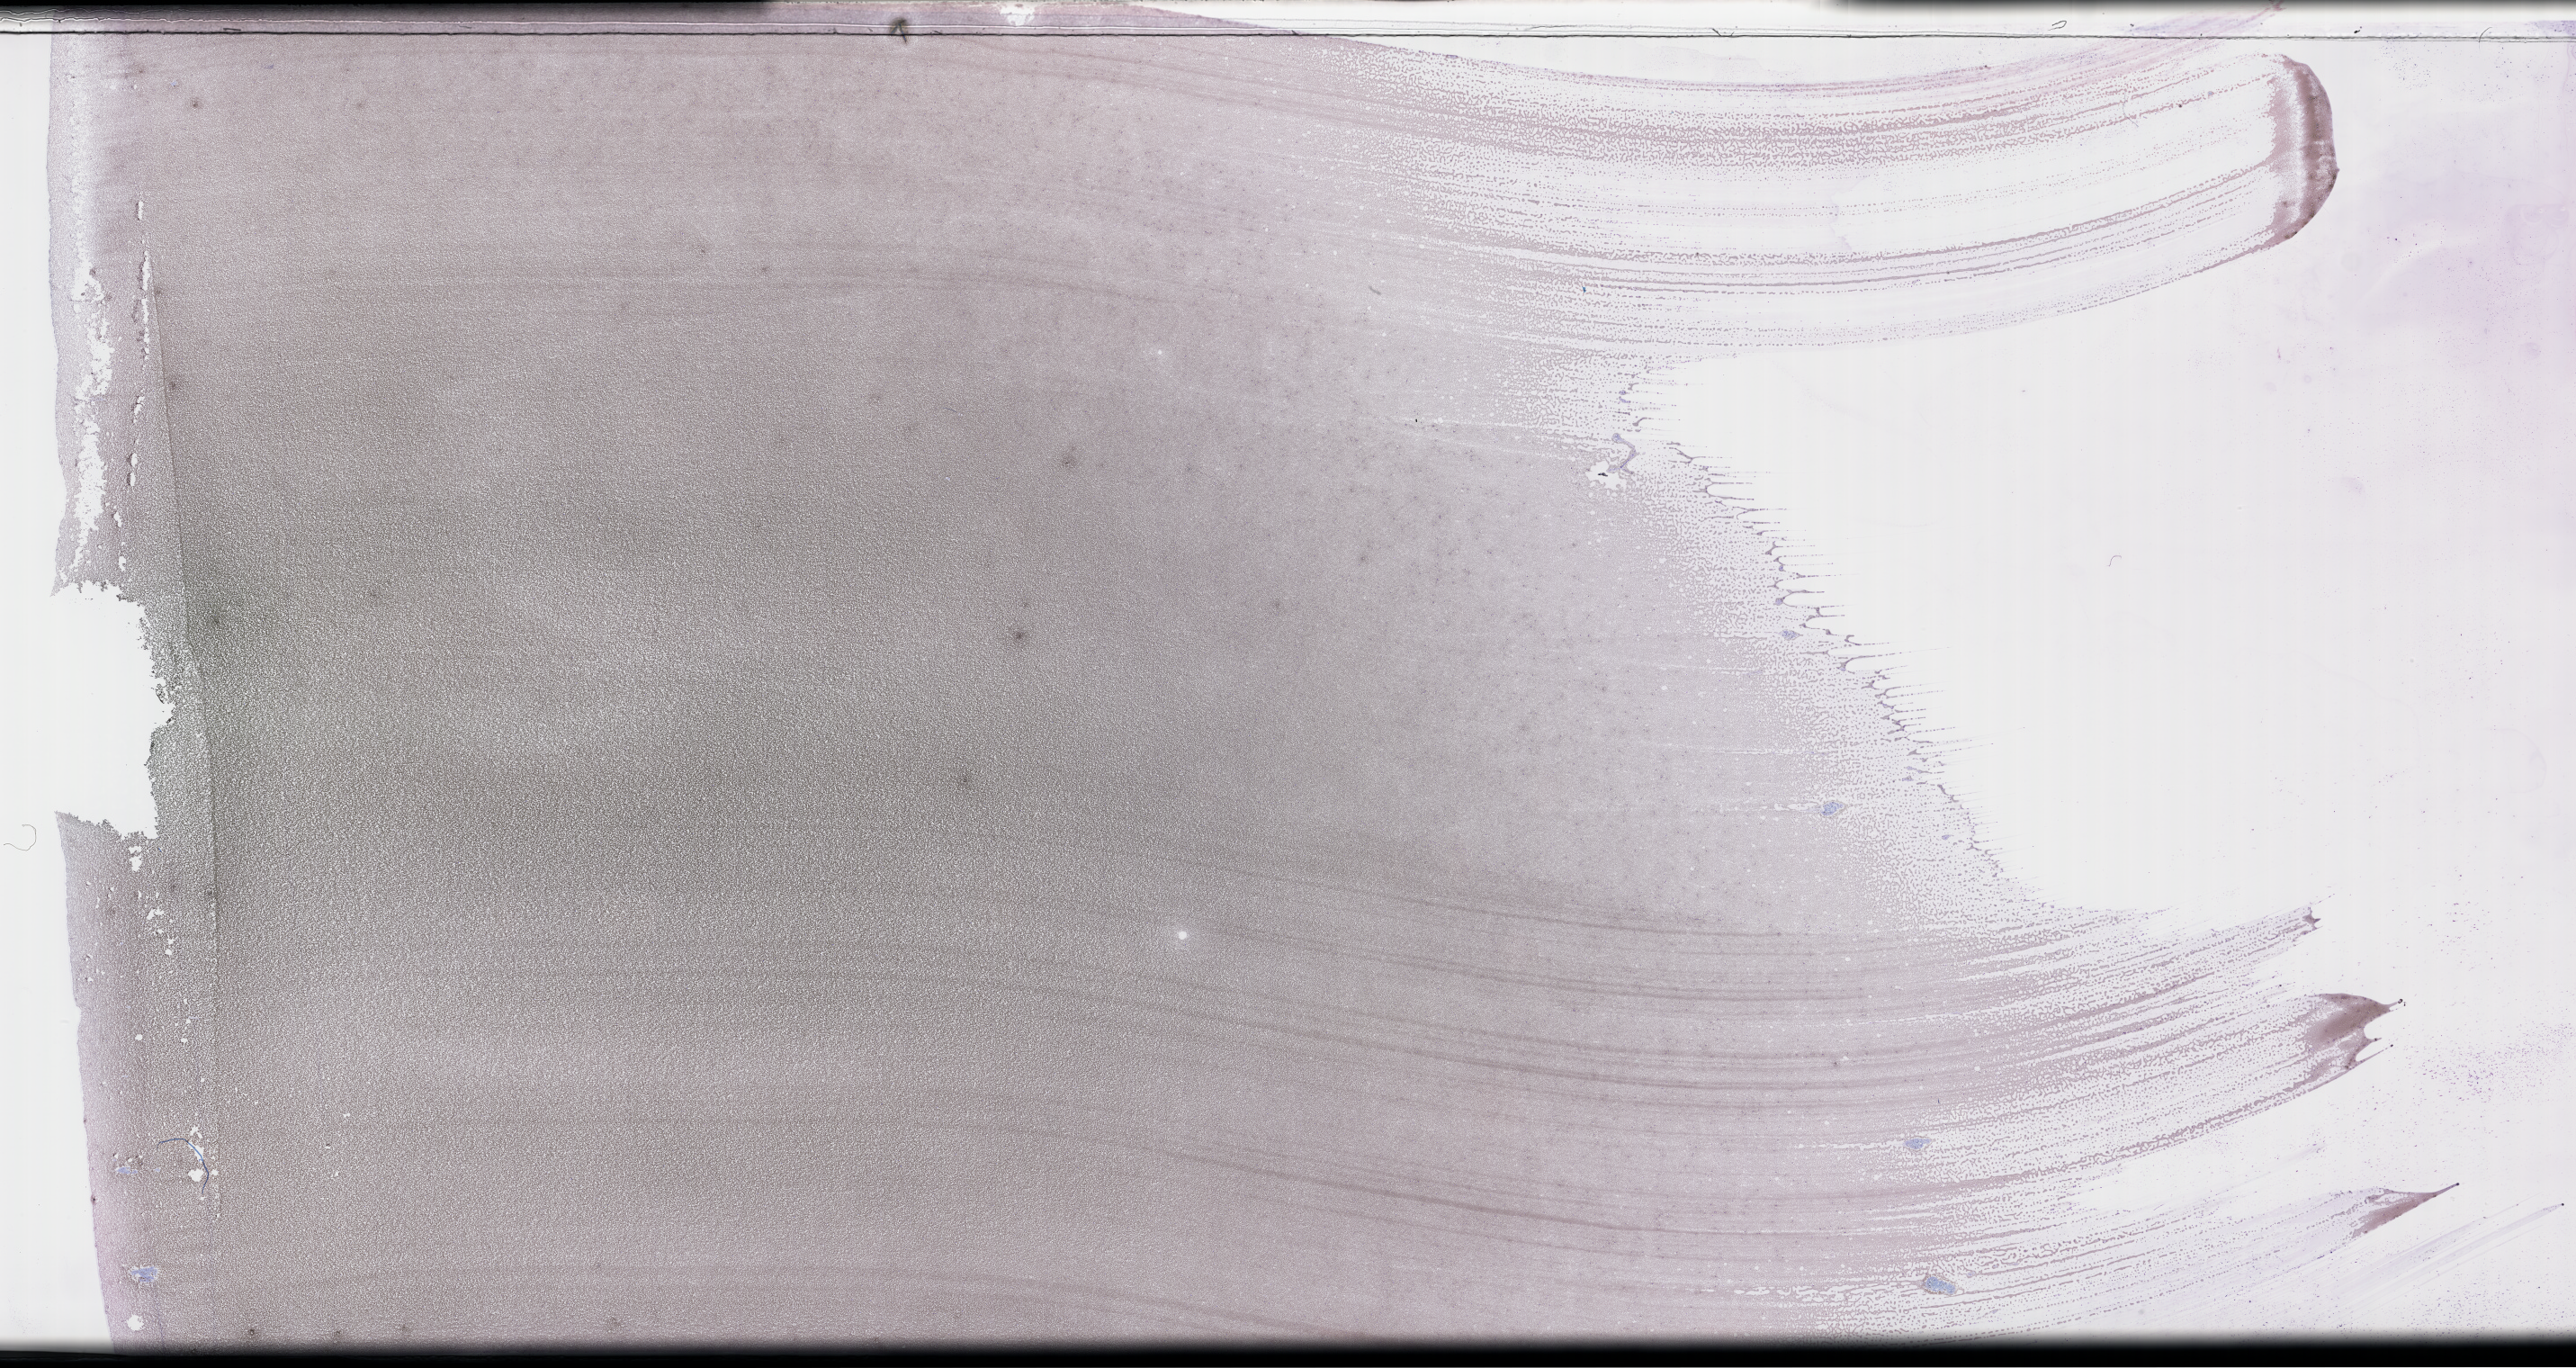
Whole-slide image of a whole blood smear, Wright–Giemsa stain, low-resolution overview of the scanned area, about 46.2 x 24.5 mm. Collected on treatment. Patient: female.
From a patient with: Plasma Cell Myeloma.